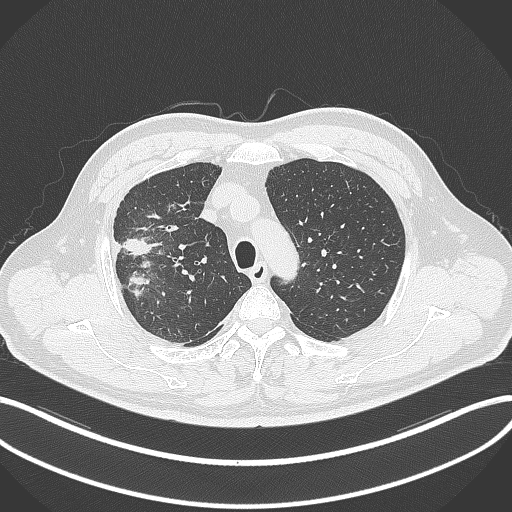
Chest CT, one axial slice; lung window (W 1500 / L -600 HU); 1 mm slice thickness; 512 × 512 image matrix. Male patient, age 55 years. From the clinical record (not read from this slice): clinical TNM (as recorded): T3 N2 M1.
Structures marked on this image (rectangle marked by the reading radiologist):
- lung tumour (recorded histology: adenocarcinoma): bounding box <118,234,161,300> (left, top, right, bottom; pixels)